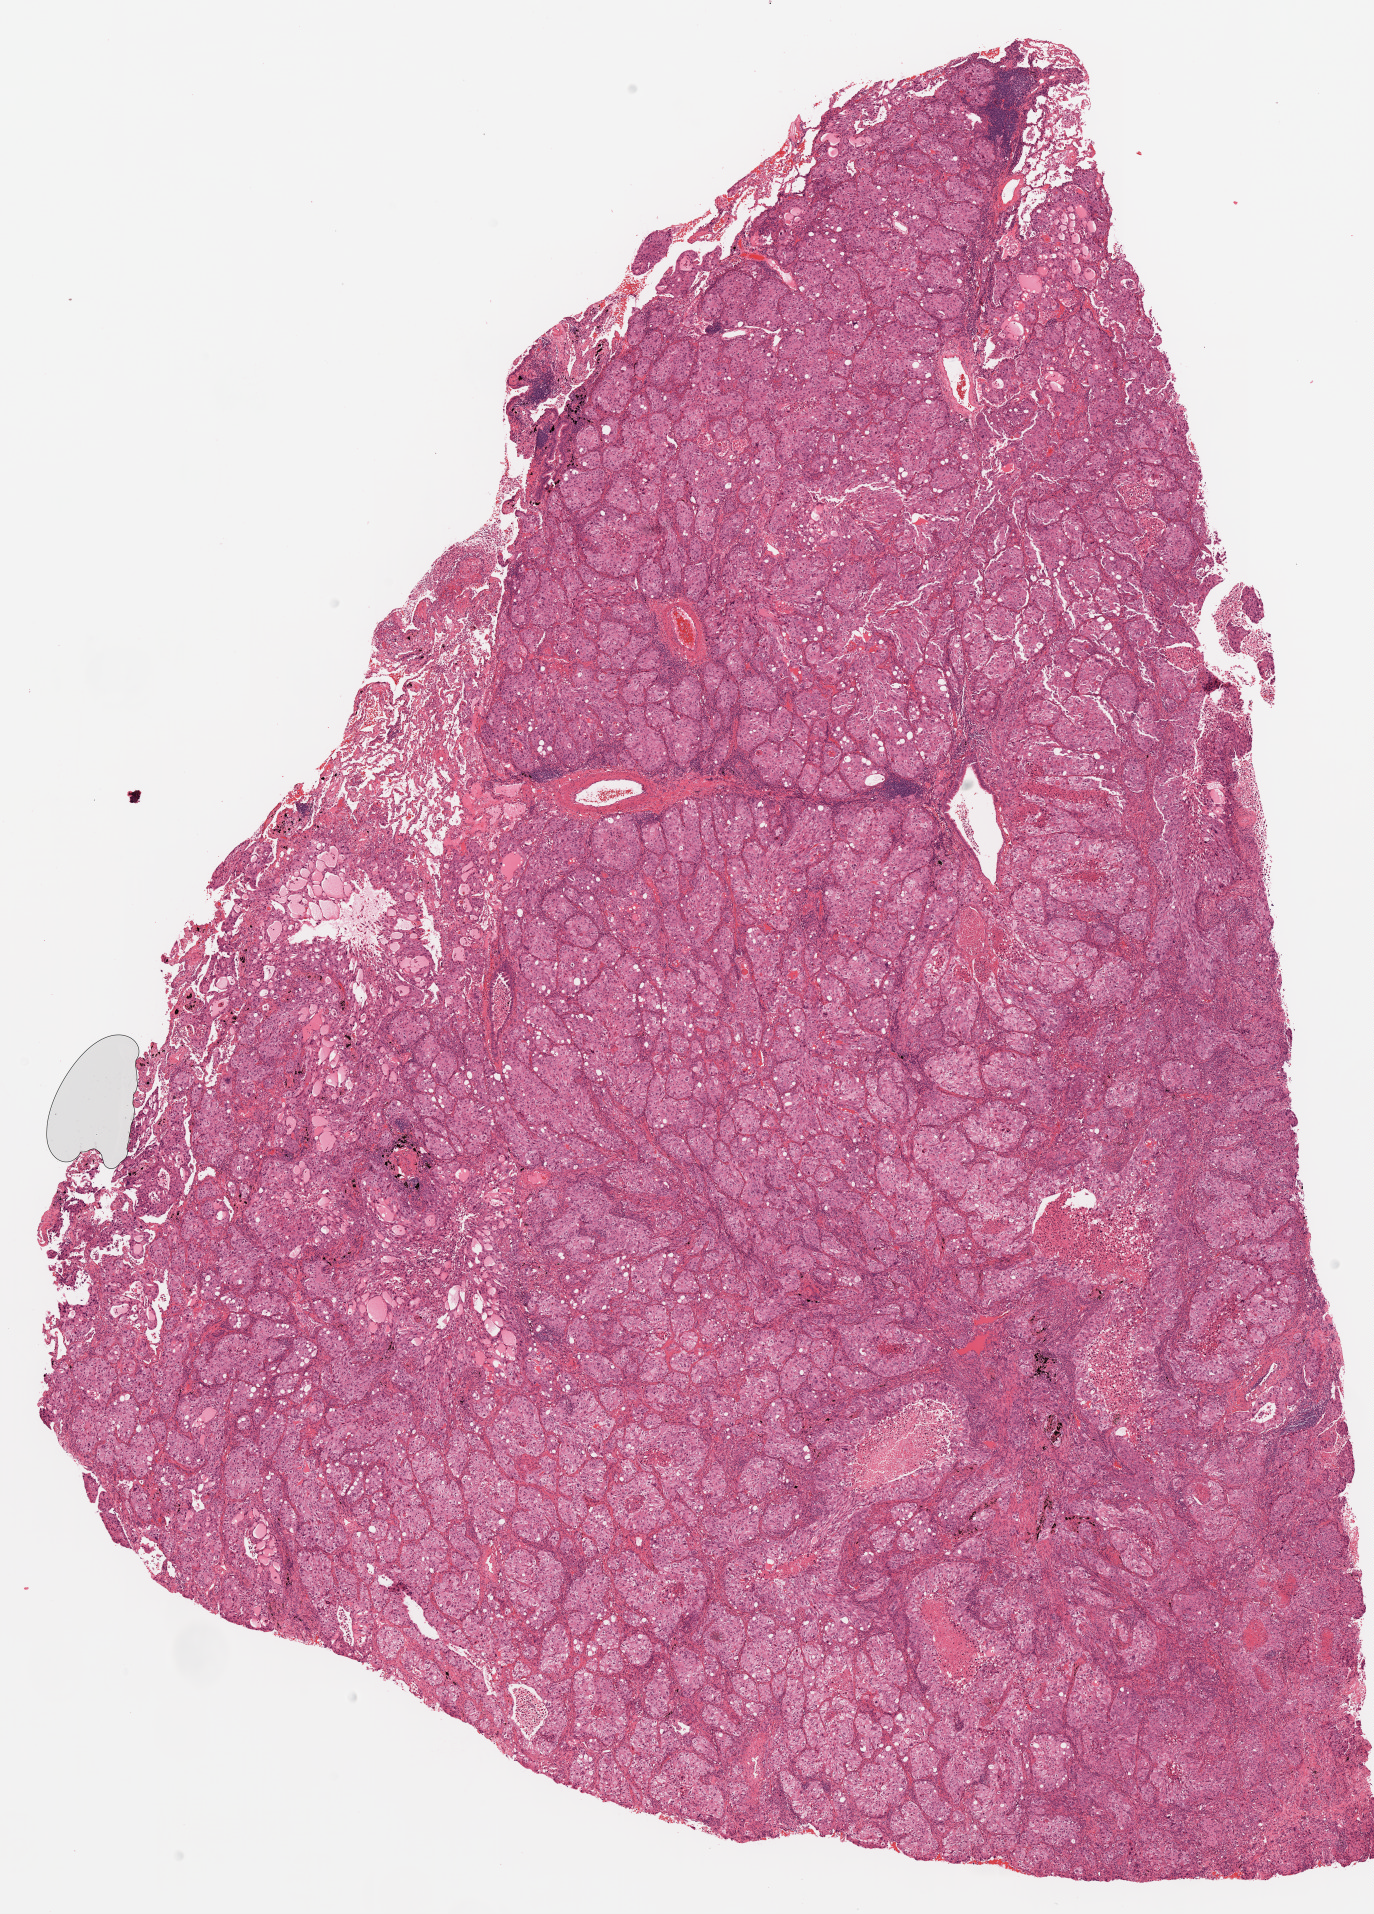
H&E whole-slide image — a low-resolution overview of the entire scanned area, about 11.0 x 15.3 mm (acquisition: 20x scan), FFPE section, sample: primary tumour, lung. Male patient.
Laterality: right. AJCC pathologic stage: IIB (6th edition). Diagnosis: Adenocarcinoma, NOS (upper lobe, lung).